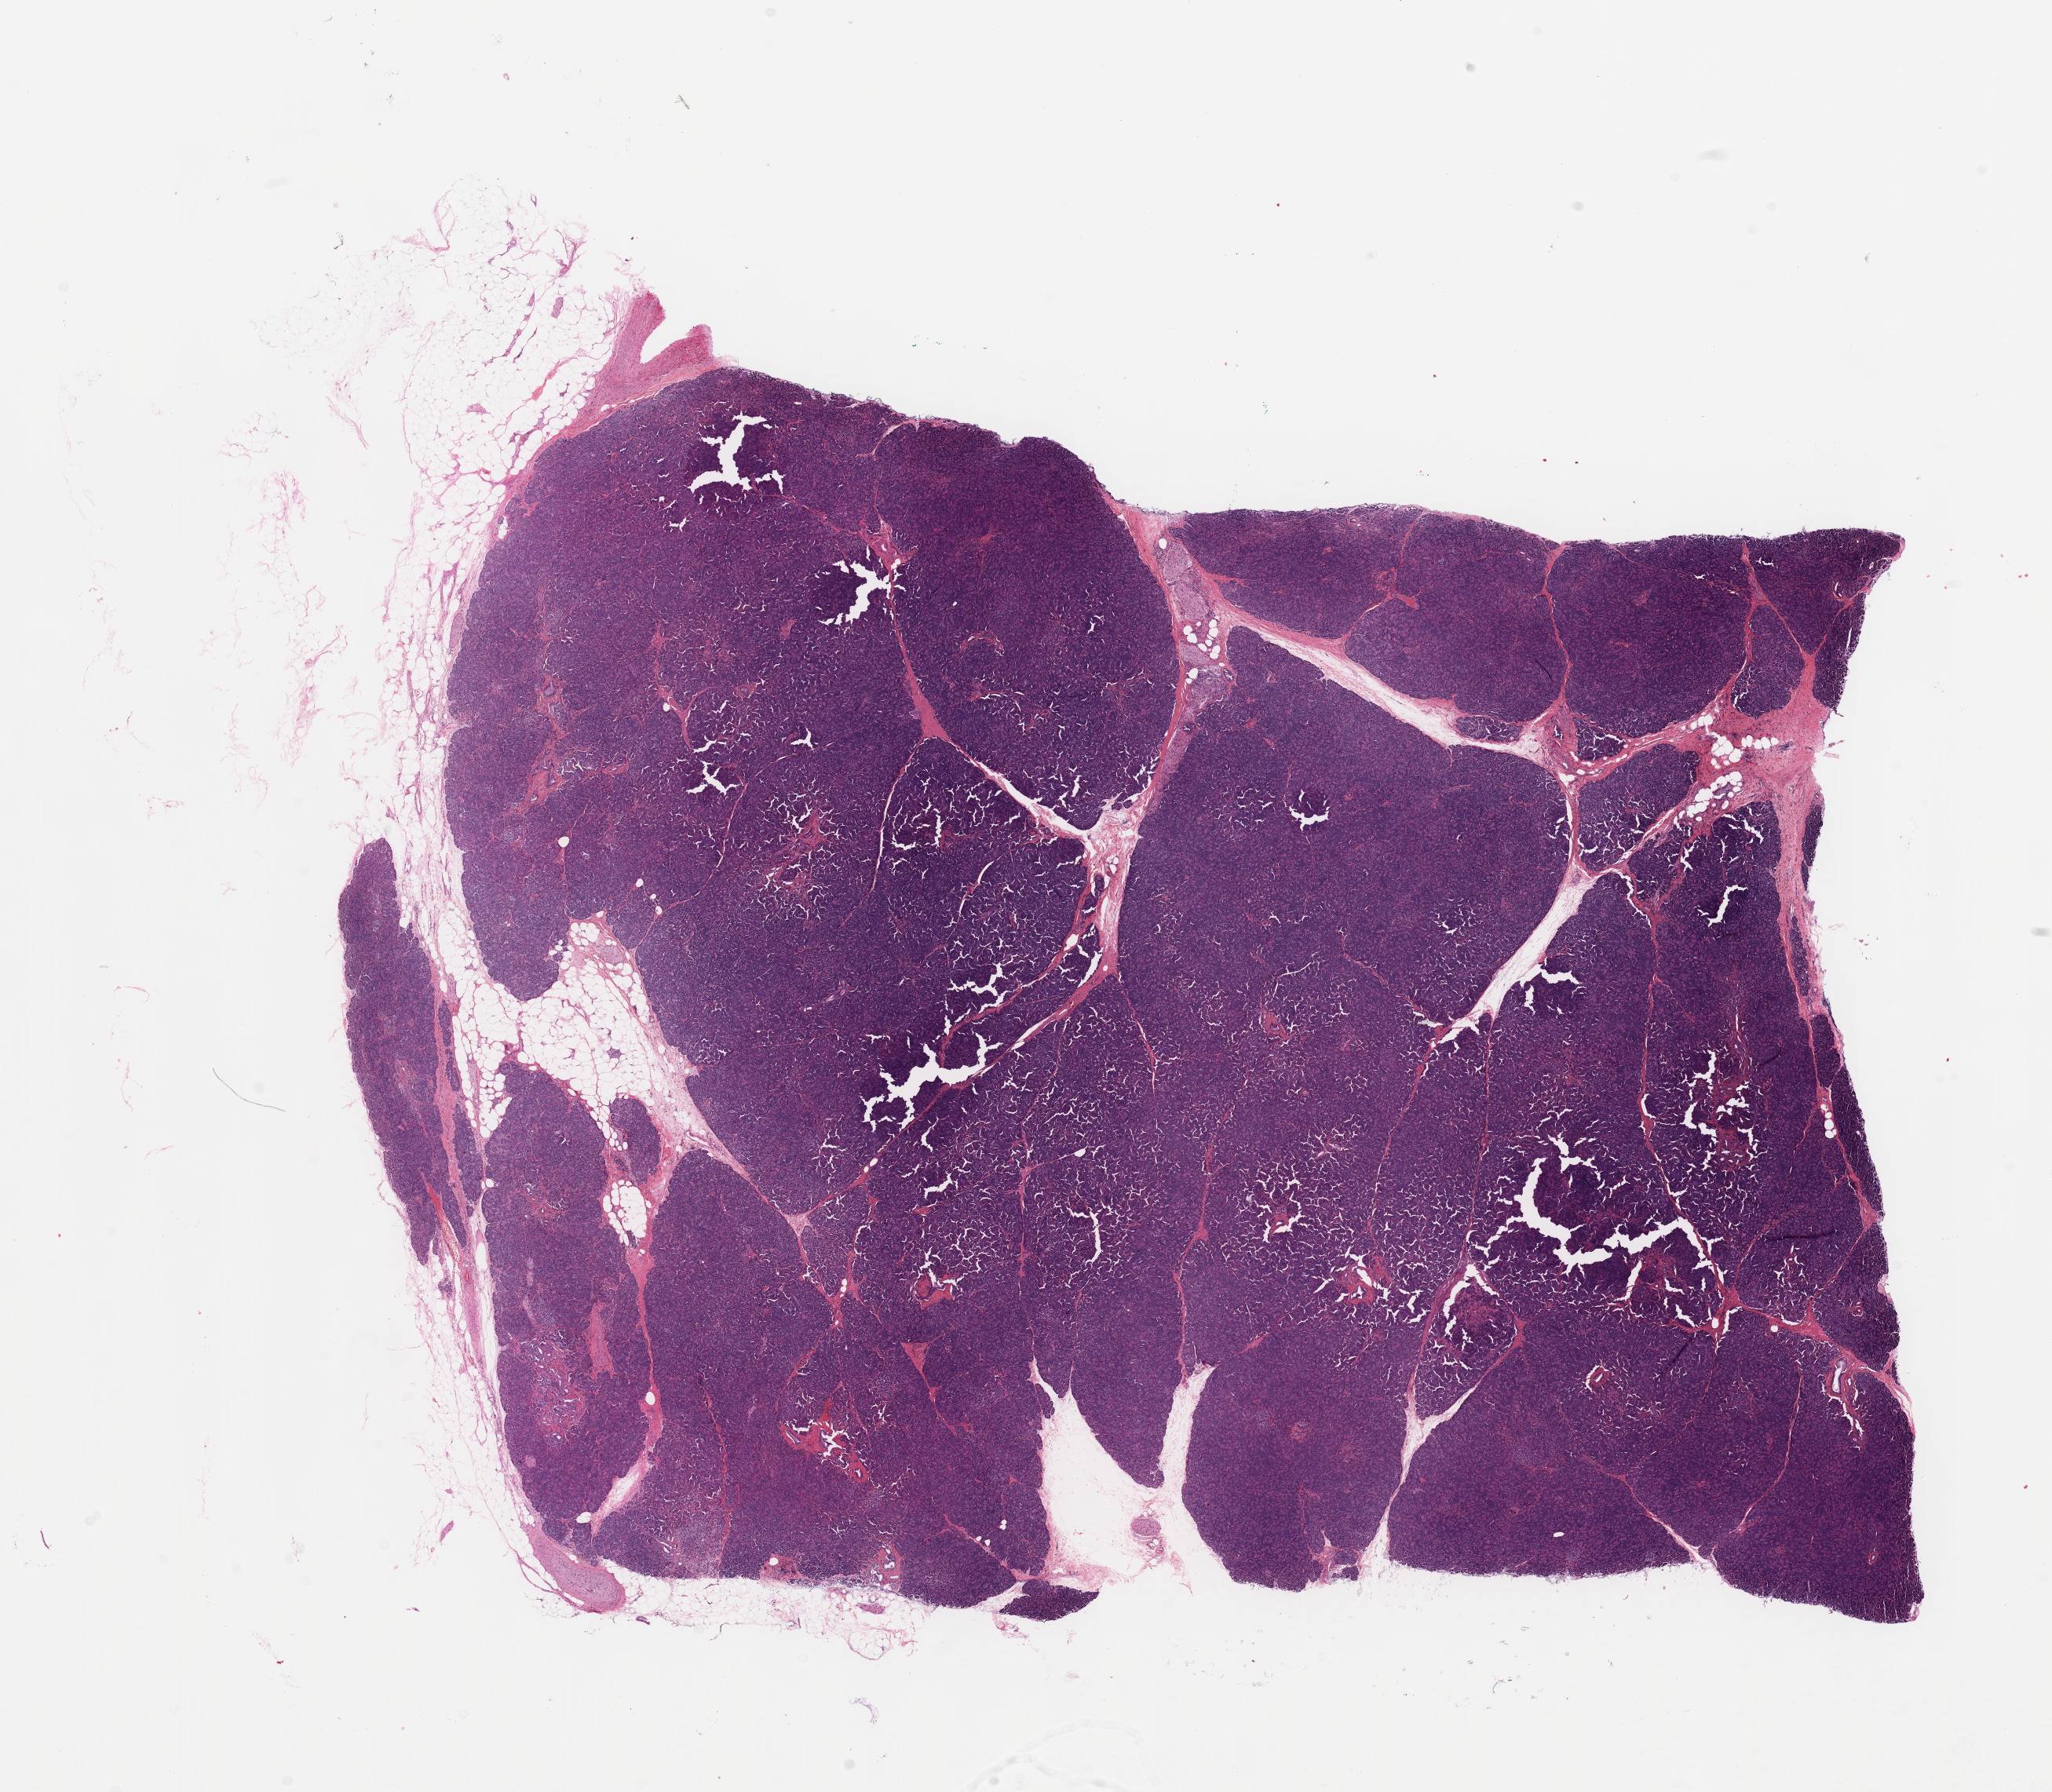
Digitized Hematoxylin and eosin (H&E) stained tissue section (whole slide) — shown as a low-resolution overview of the whole scanned area (about 20.7 x 18.1 mm). Normal (non-tumour) tissue sample, sampled site: pancreas. Patient: male, age 42 years.
This section: normal (non-tumour) tissue from the same patient. Patient diagnosis: Infiltrating duct carcinoma, NOS.